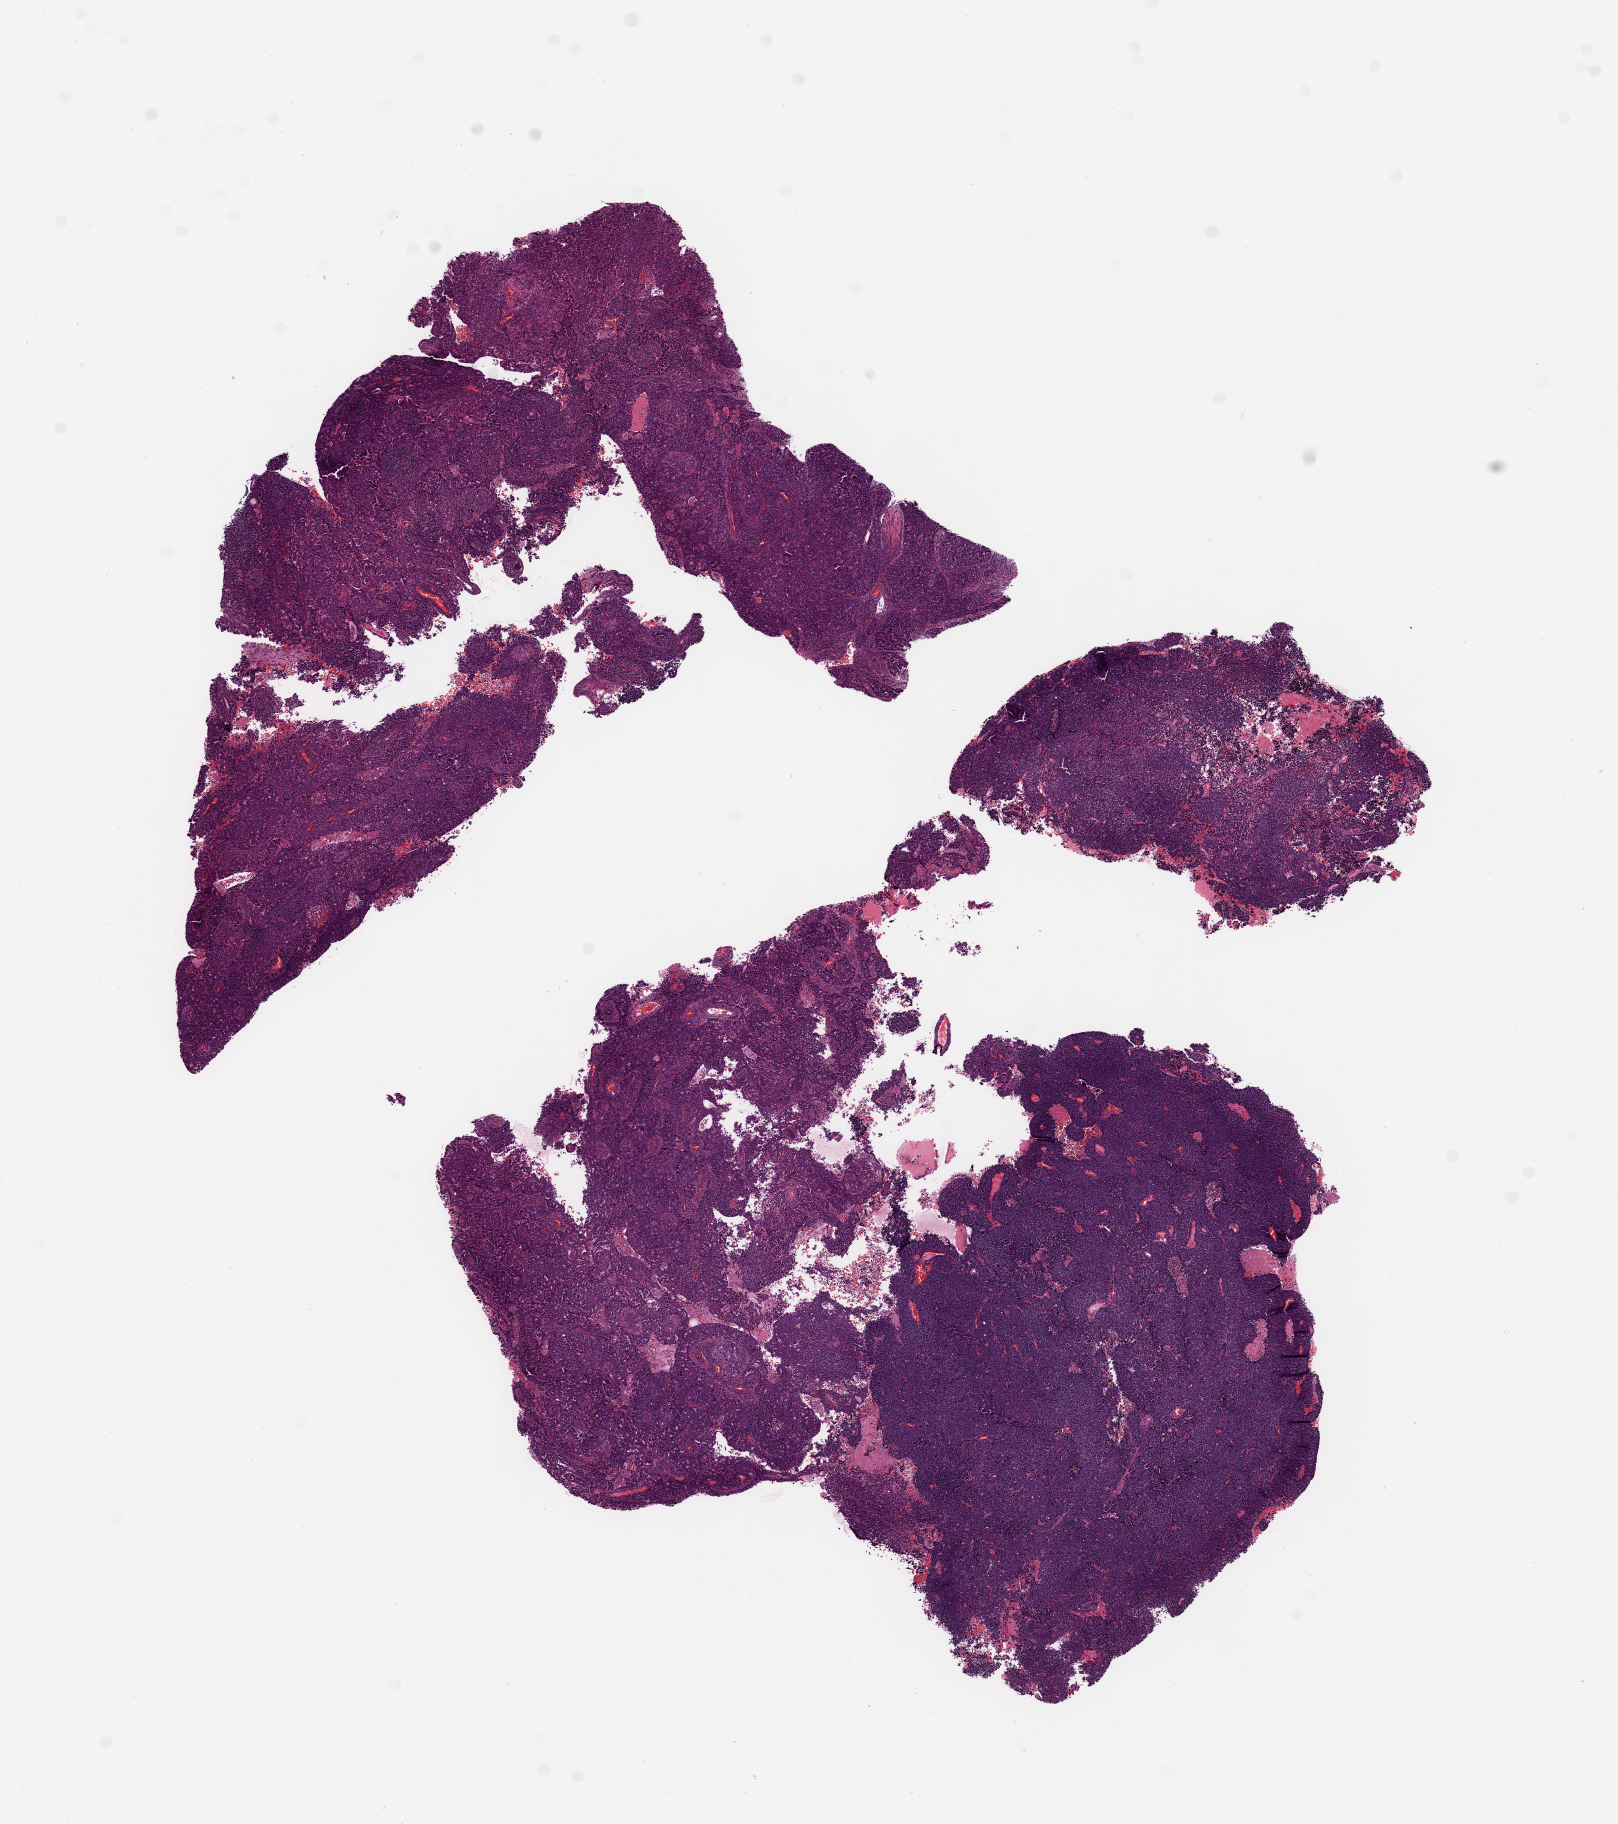
Digitized Hematoxylin and eosin (H&E) stained tissue section (whole slide), a low-resolution overview of the entire scanned area, about 12.8 x 14.4 mm, uterus, tumour tissue. Patient: female, aged 90 or older. Histologic grade: G3 (poorly differentiated).
AJCC pathologic stage: I. Diagnosis: Endometrioid adenocarcinoma, NOS.